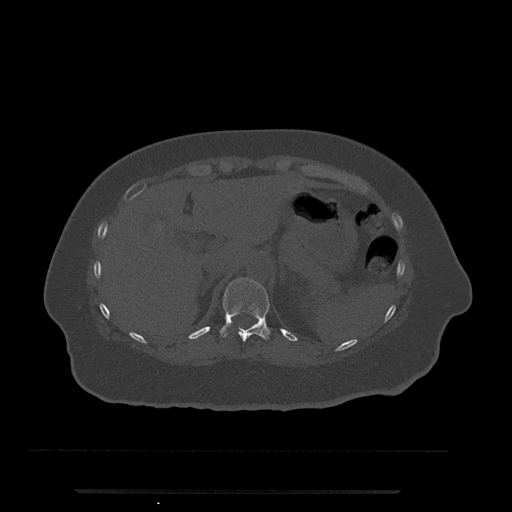
CT including the spine, one axial slice; slice 228 of 797 in the series (ordered by position); reconstruction kernel Br40s/3; bone window (W 1800 / L 400 HU); 512 × 512 image matrix, field of view 440 × 440 mm. Female patient, age 51 years. From the clinical record (not read from this slice): primary cancer: neuro.
Annotated regions visible in this slice (semi-automatic segmentation, software-assisted and operator-edited):
- T11 vertebra: bounding box <219,278,270,342> (left, top, right, bottom; pixels)